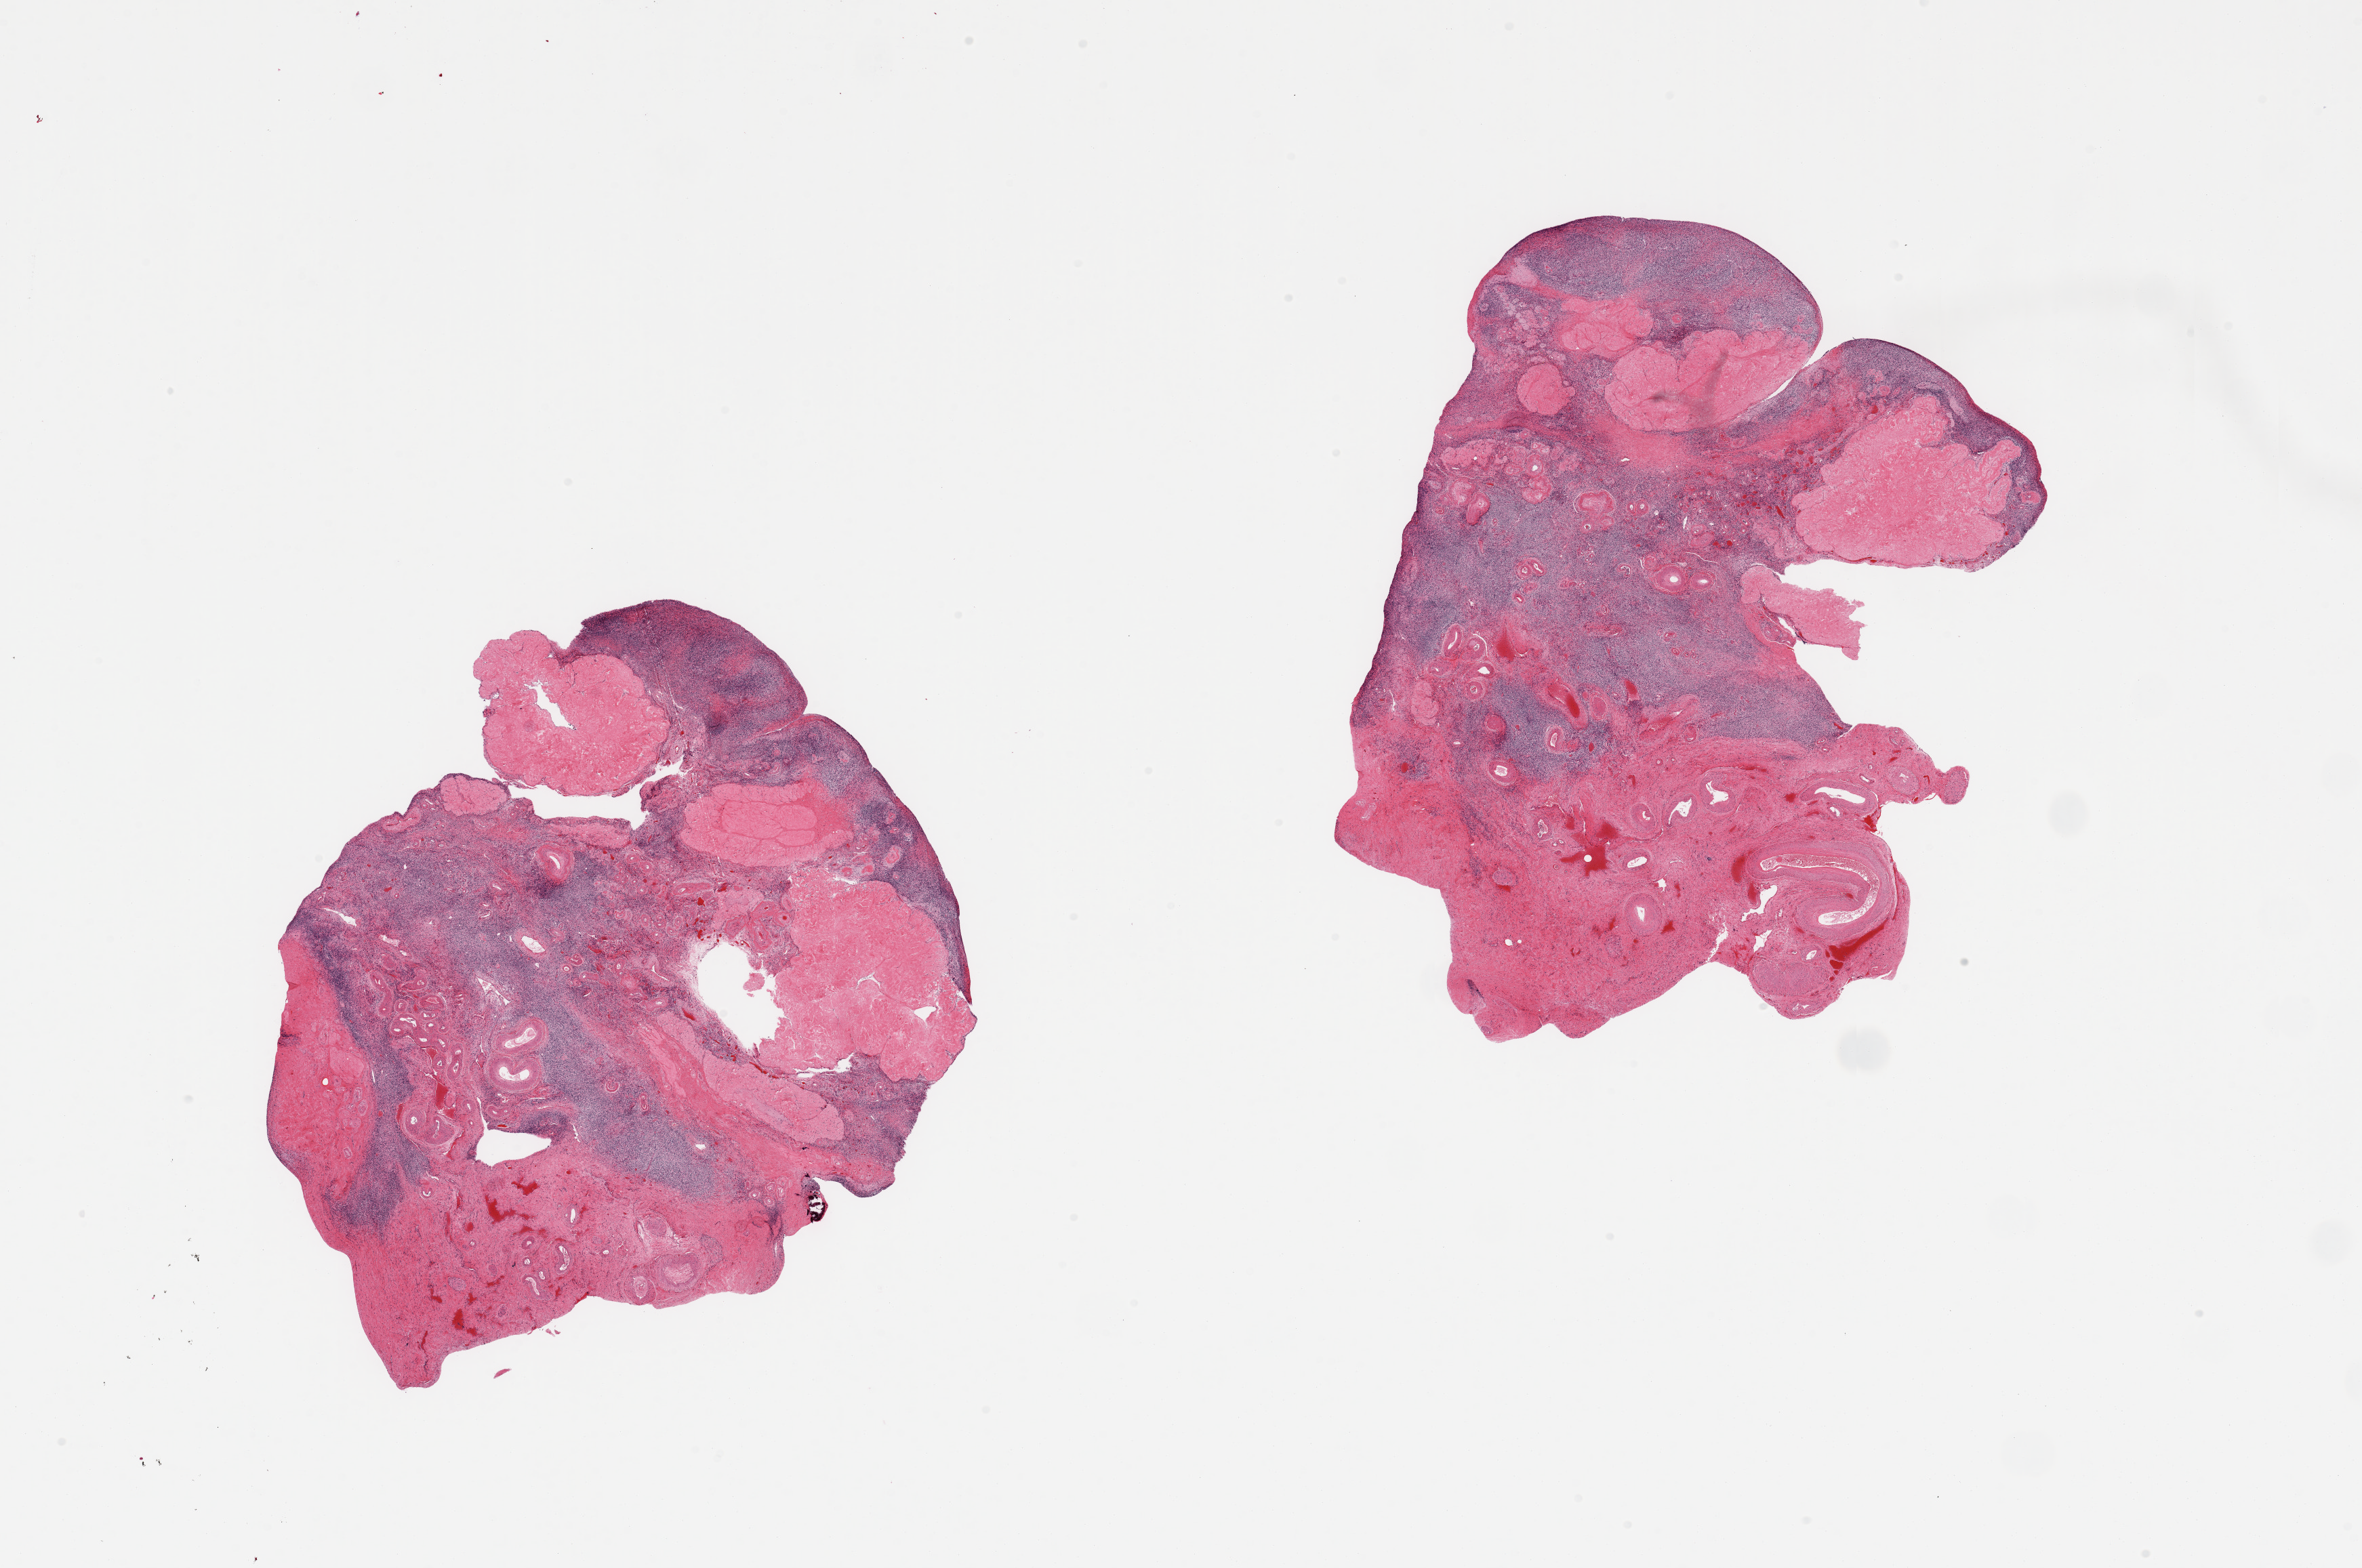
Whole-slide image, haematoxylin and eosin stain, brightfield, low-resolution overview of the scanned area, about 27.6 x 18.3 mm (from a 20x scan), PAXgene-fixed paraffin-embedded (PFPE) section, section of ovary (target tissue), tissue donor sample. Female donor.
Review note (as recorded): 2 pieces, post menopausal atrophy.